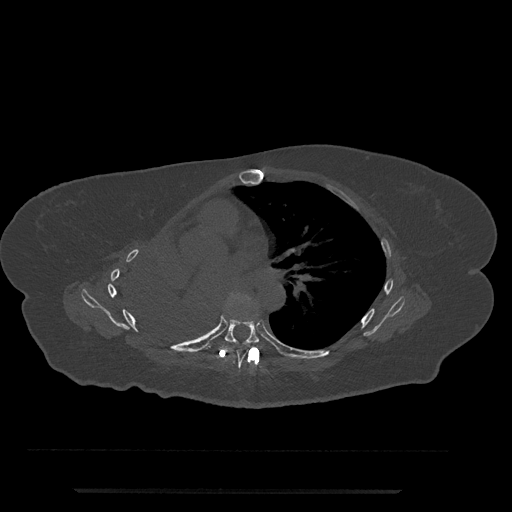
CT including the spine, one axial slice. Reconstruction kernel Br40s/3. 120 kVp. Bone window (W 1800 / L 400 HU). 0.5 mm slice thickness. 512 × 512 image matrix. Female patient, age 51 years. From the clinical record (not read from this slice): primary cancer: neuro.
Annotated regions visible in this slice (semi-automatically segmented with operator editing):
- T6 vertebra: box from (x=224, y=346) to (x=253, y=370) px
- T7 vertebra: (x=225, y=315)–(x=260, y=345)